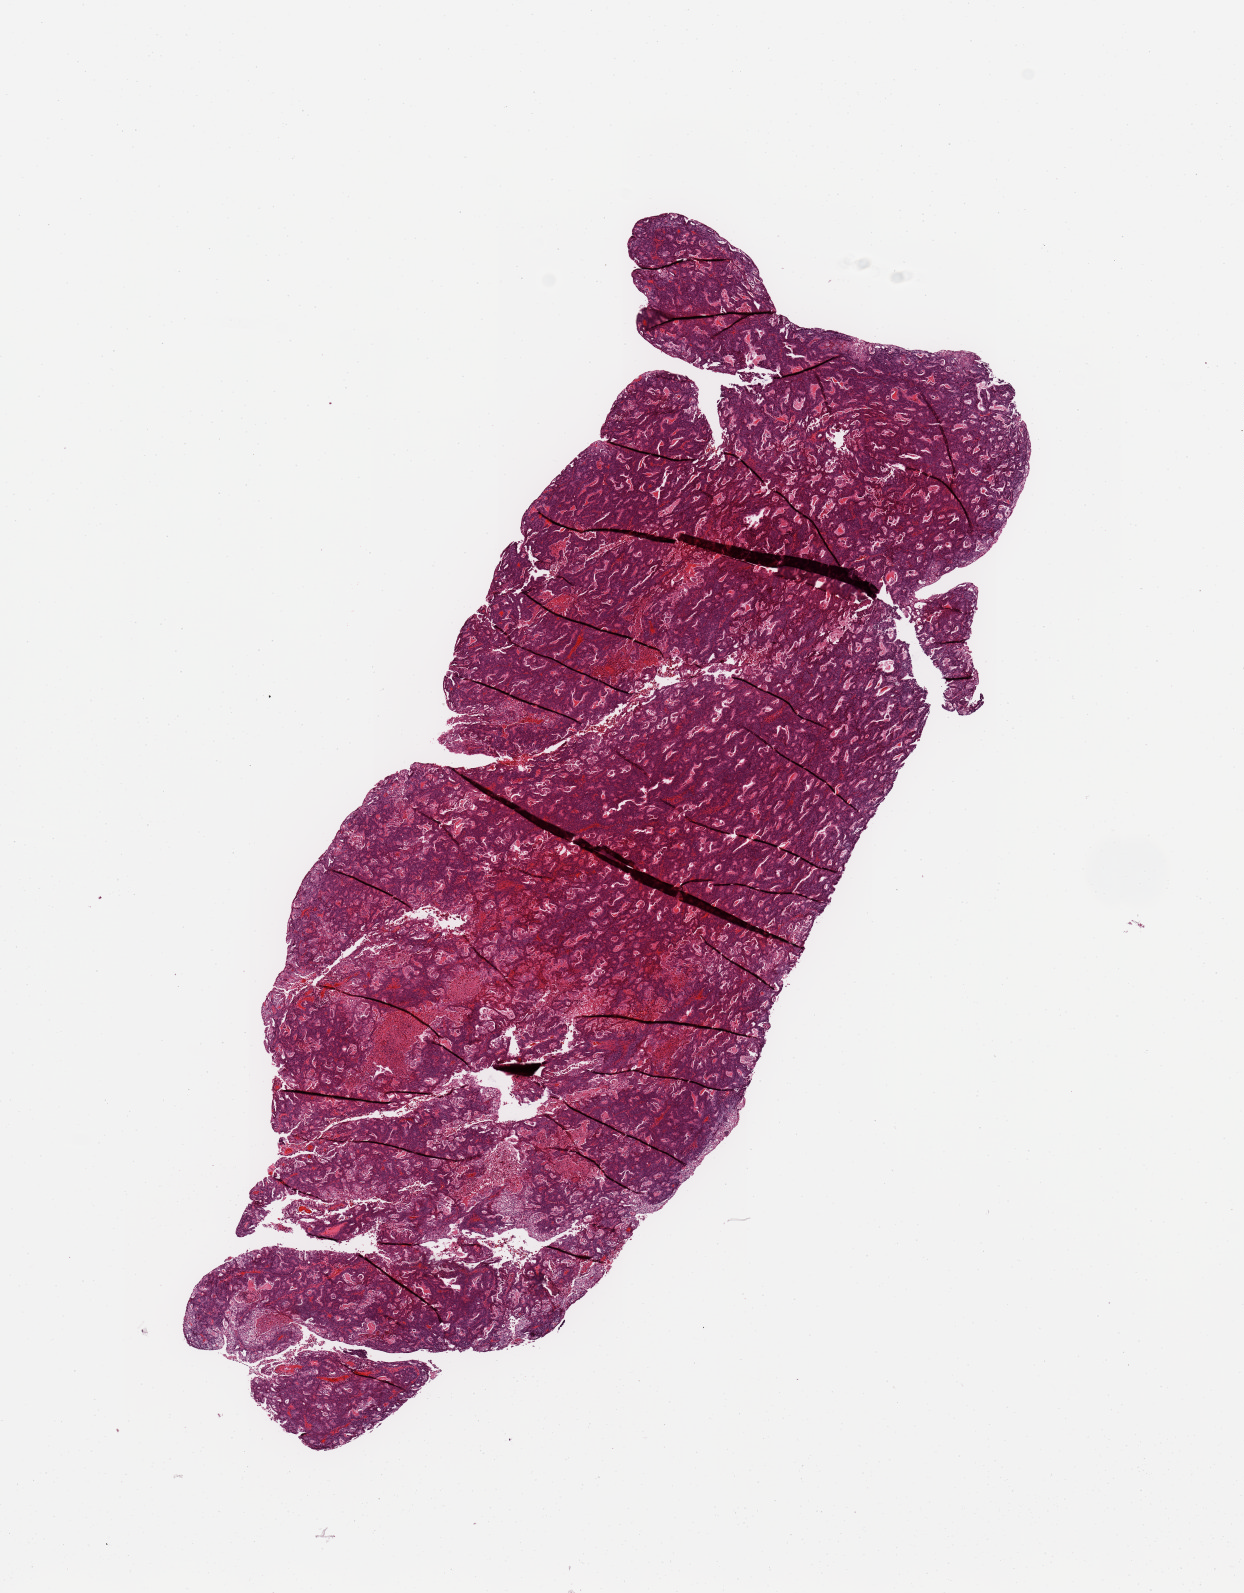
Hematoxylin and eosin (H&E) stained whole-slide image — low-resolution overview of the scanned area, about 9.8 x 12.6 mm, uterus, tumour tissue. 55-year-old female patient. Histologic grade: G1 (well differentiated).
Histologic diagnosis: Endometrioid adenocarcinoma, NOS. AJCC pathologic stage: III.